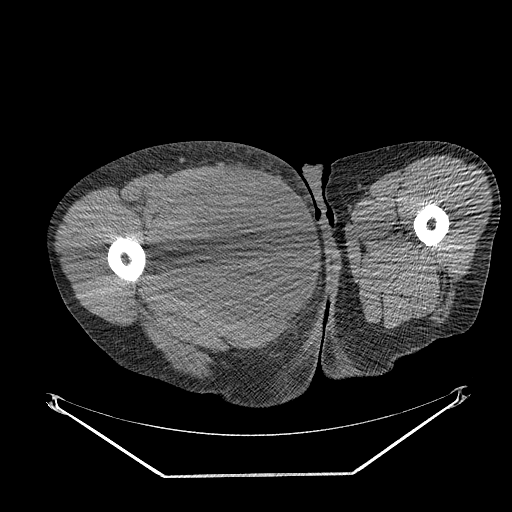
CT of an extremity soft-tissue mass (from a PET/CT study), one axial slice. Slice 268 of 311 in the series (ordered by position). Reconstruction kernel STANDARD. Soft-tissue window (W 400 / L 40 HU). 3.75 mm slice thickness. 512 × 512 image matrix, field of view 500 × 500 mm. Male patient. From the clinical record (not read from this slice): histological type: undifferentiated - pleiomorphic; grade: high; site of the primary tumour: right thigh.
Structures marked on this image (expert contour drawn on MRI and transferred to this co-registered scan by the dataset authors):
- gross tumour volume including surrounding oedema: bounding box <157,171,268,279> (left, top, right, bottom; pixels)
- gross tumour volume (mass): <158,171,268,279>